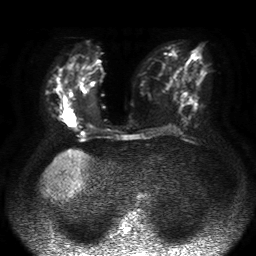
Breast MRI, one axial slice. Diffusion-weighted series; image 2 of 4 stored at this slice position (different b-values; order by instance number). 1.5 T. 4 mm slice thickness. 256 × 256 image matrix. Female patient.
Structures marked on this image (manually delineated by an expert):
- tumour on diffusion-weighted imaging: bounding box <64,114,79,126> (left, top, right, bottom; pixels)